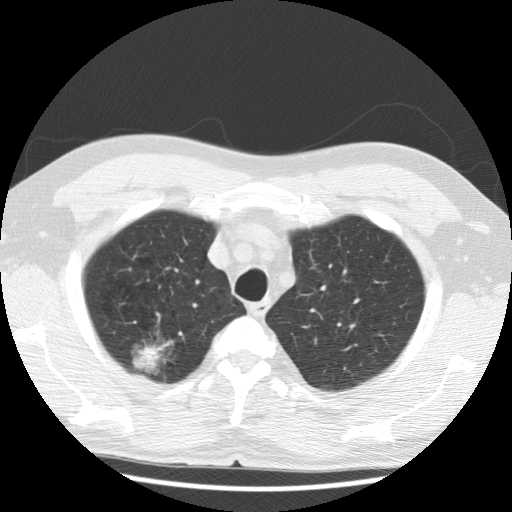
Chest CT (low-dose screening protocol), one axial image, baseline annual screen, lung window (W 1500 / L -600 HU), slice 25 of 122 in the series, 512 × 512 image matrix. Male, age 59 years at enrolment. Former smoker at enrolment.
Expert reader's lesion annotation, box from (x=118, y=326) to (x=180, y=385) px. The exam's reader record, not a measurement of the box and not confirmed to be the same lesion: non-calcified nodule or mass ≥4 mm, right upper lobe, 30 × 28 mm, poorly defined margins, ground glass attenuation. Later outcome: lung cancer diagnosed 40 days after this screen — bronchiolo-alveolar carcinoma, non-mucinous, right upper lobe, well differentiated (G1), stage IA (AJCC 6th edition), 15 mm at pathology.